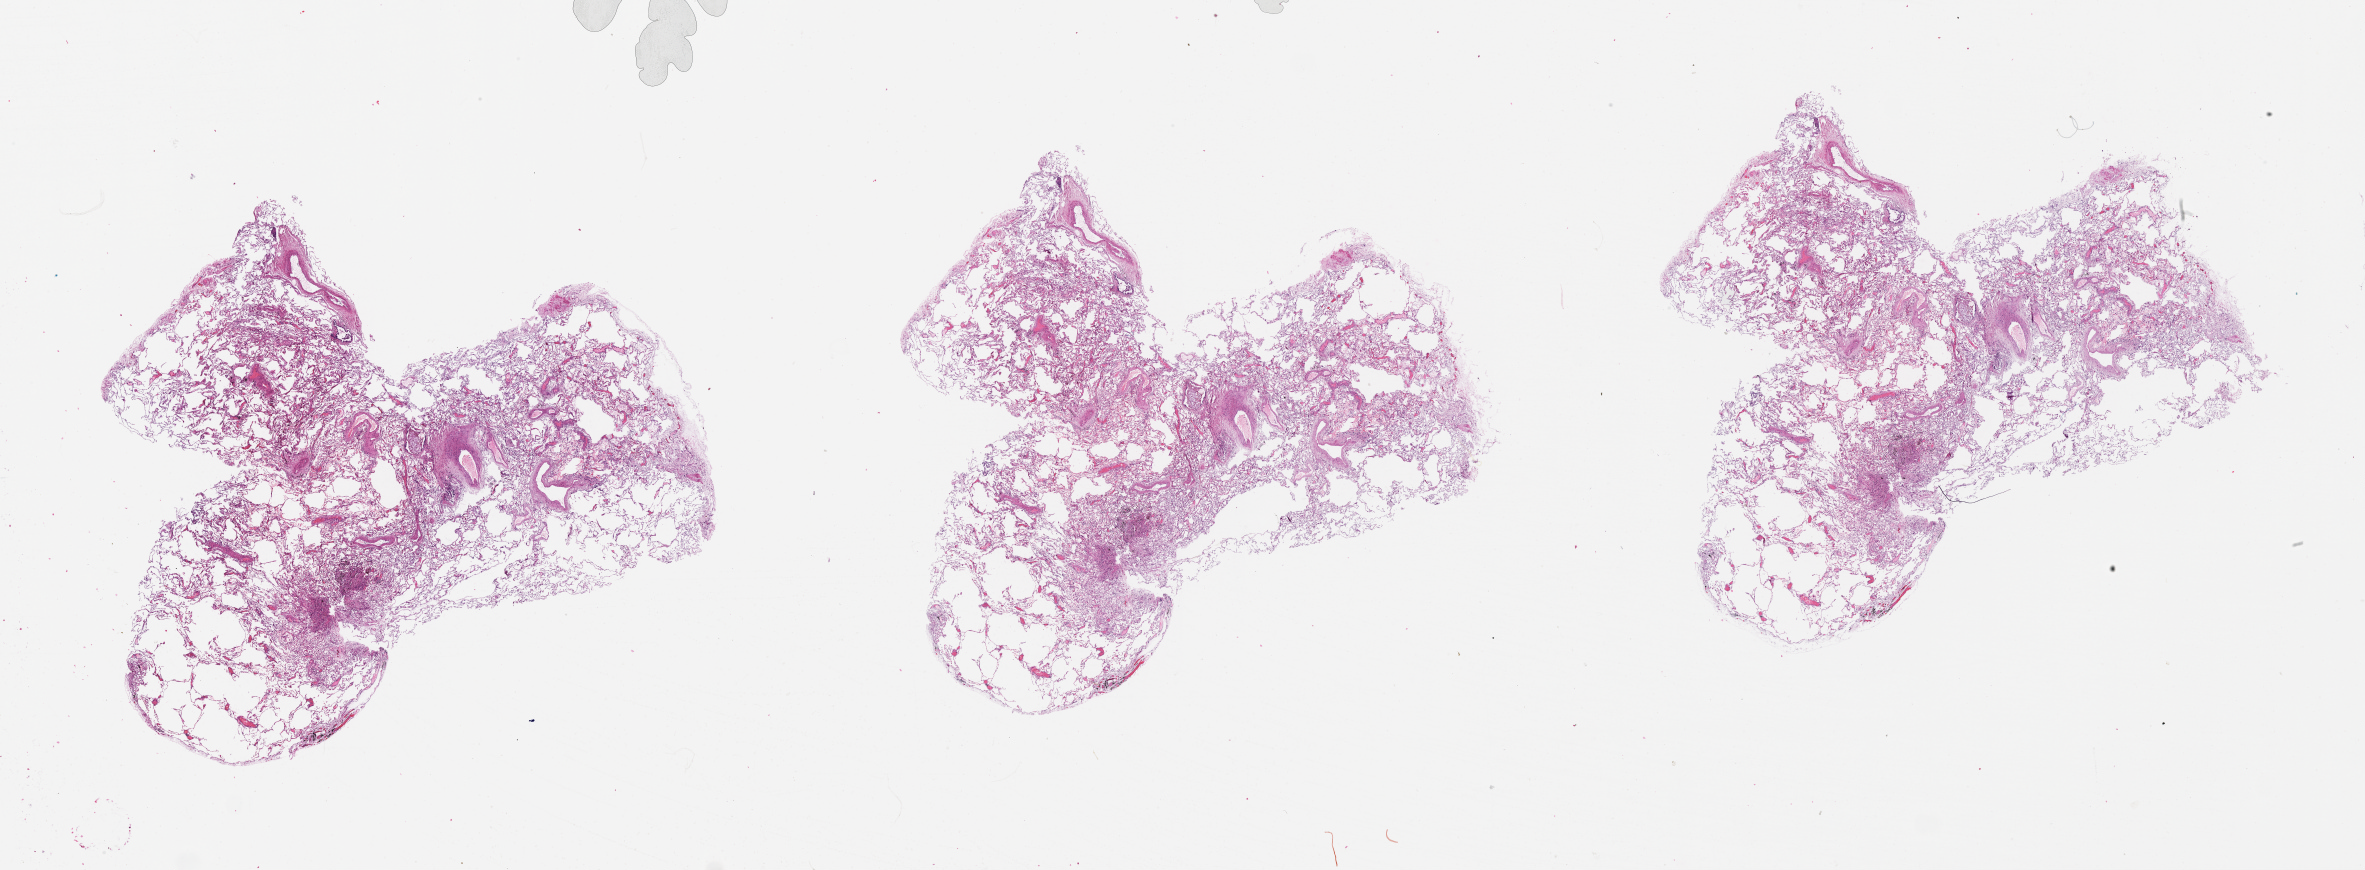
Whole-slide histology image, H&E, low-resolution overview of the scanned area, about 38.1 x 14.0 mm, lung, tissue type not recorded.
• patient diagnosis (cohort enrolment): lung adenocarcinoma (lung)